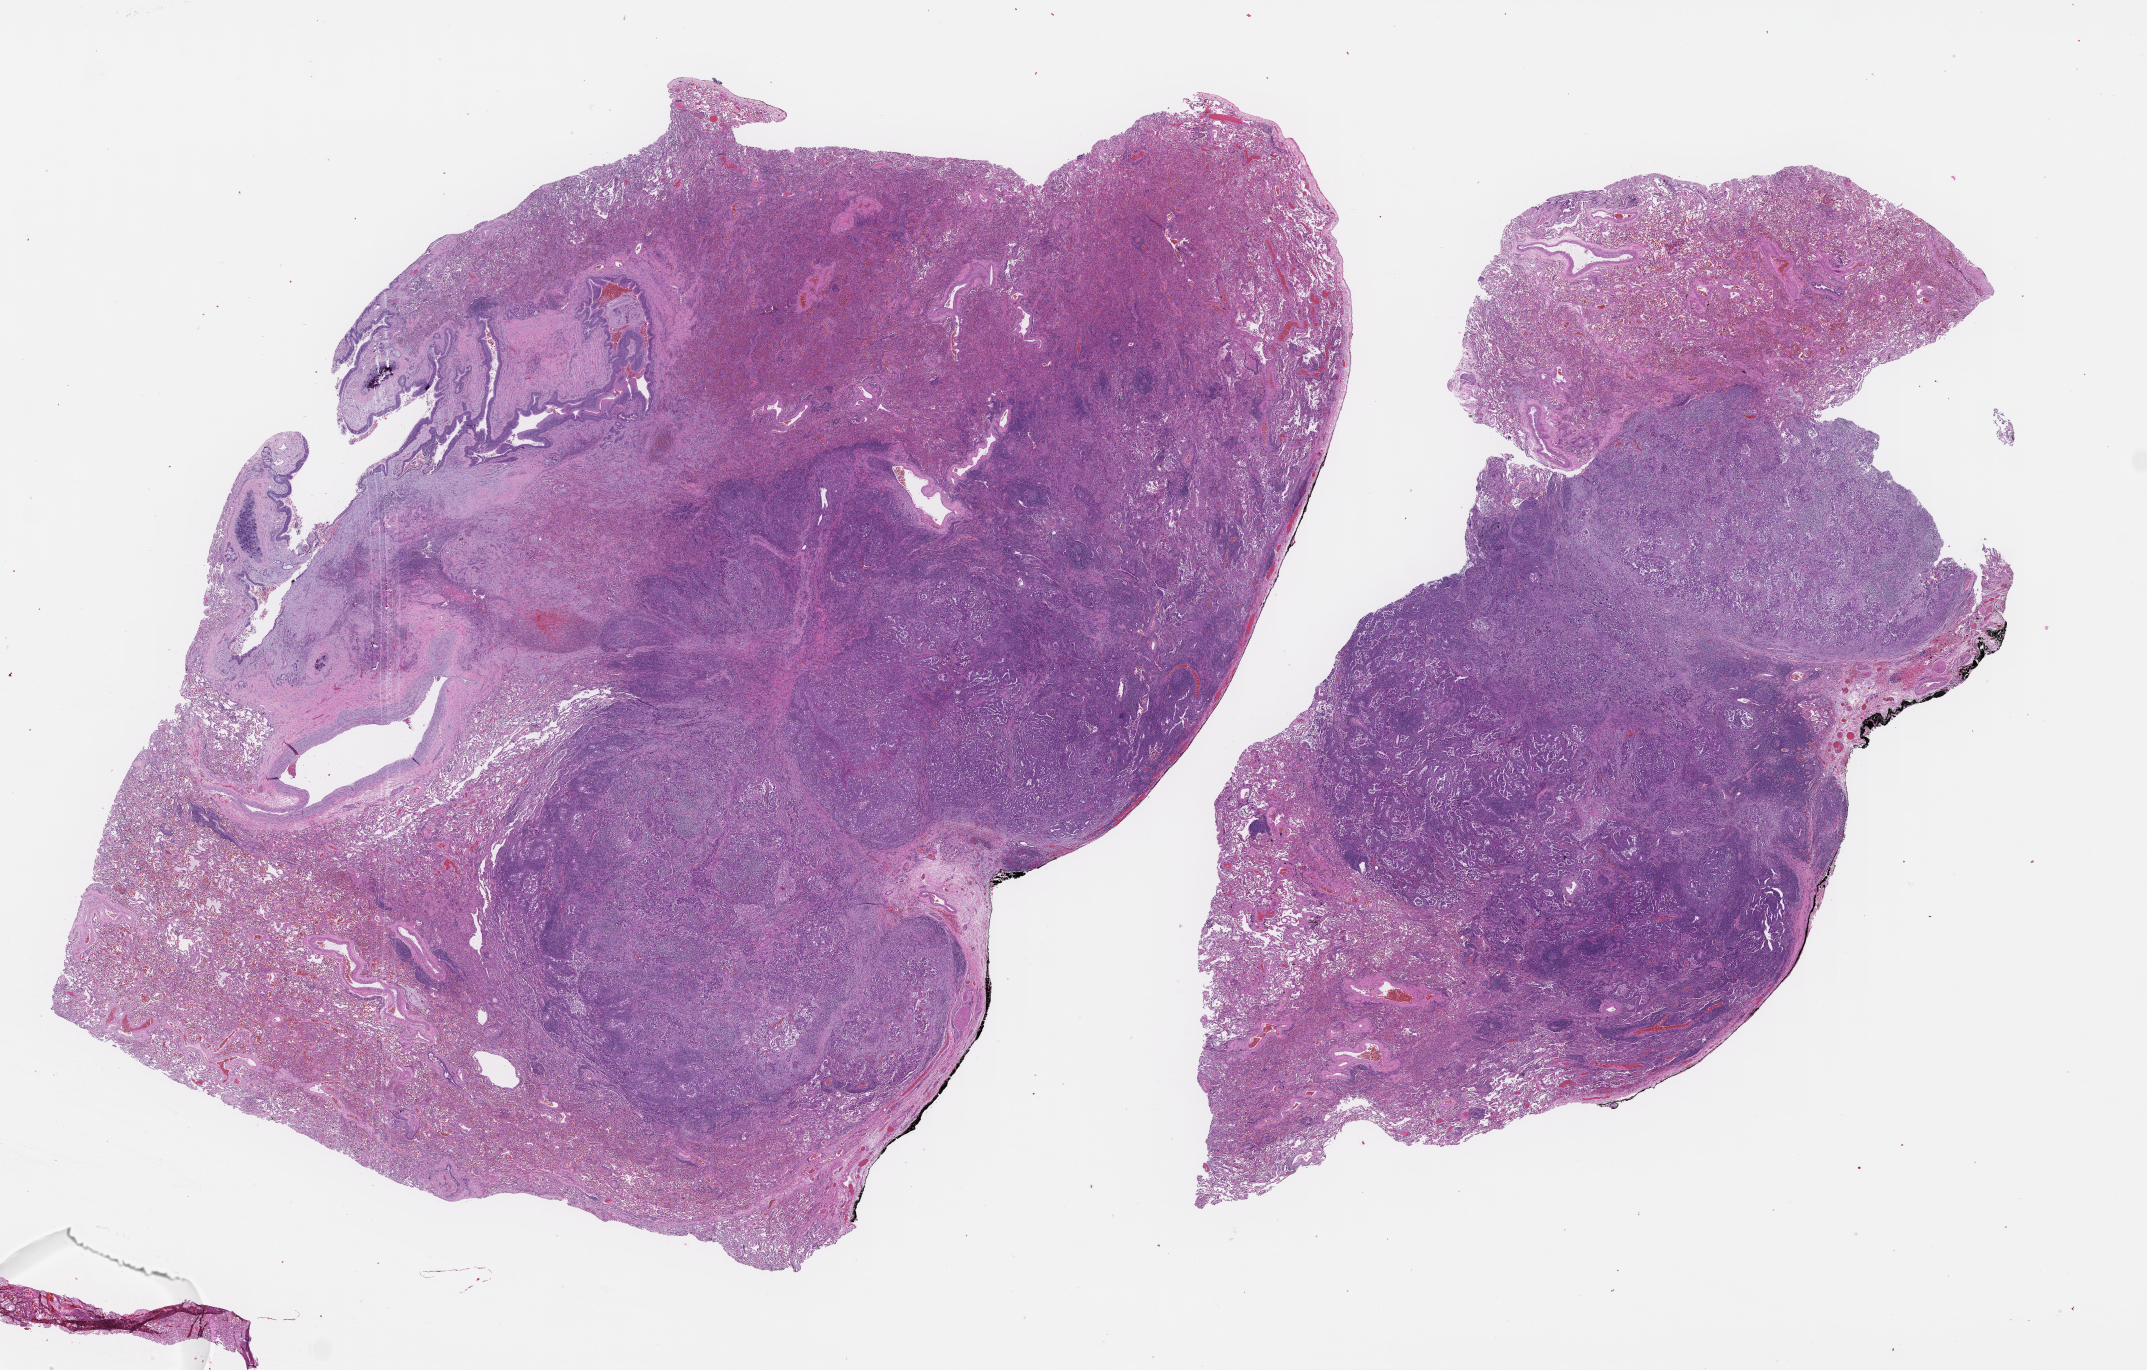
Haematoxylin and eosin whole-slide image, shown as a low-resolution overview of the whole scanned area (about 34.7 x 22.1 mm). Formalin-fixed paraffin-embedded section. Tissue site: lung. Female patient.
- this section: primary tumour tissue
- diagnosis: Non-Small Cell Lung Carcinoma